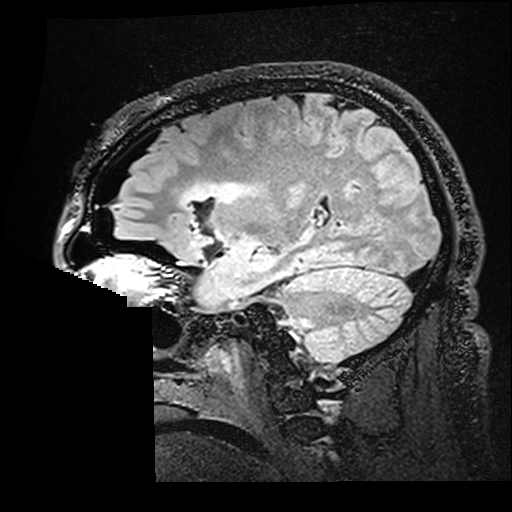
Brain MRI from a brain-tumour surgery series, one sagittal slice; position 115 of 176 along the scan axis; T2 FLAIR; 512 × 512 image matrix. From the clinical record (not read from this slice): histopathology: Astrocytoma; WHO grade: 2; IDH mutation: yes; tumour location: Right Insular.
Structures marked on this image (outlined manually by an expert reader):
- residual tumour: box from (x=180, y=182) to (x=245, y=208) px